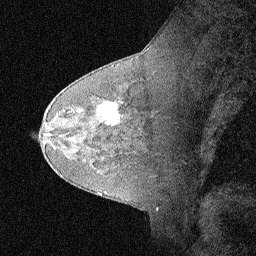
Breast MRI (dynamic contrast-enhanced), one sagittal slice; slice 43 of 64 in the series (ordered by position); dynamic contrast-enhanced study with each time point stored as its own series, time point 2 of 3 at this slice position (early post-contrast, ordered by acquisition time); 1.5 T; TE 4.5 ms, TR 11 ms; 2.06 mm slice thickness; 256 × 256 image matrix, field of view 200 × 200 mm. Female patient, age 62 years. Case-level facts recorded for this patient, not image findings: setting: breast cancer imaged before/during neoadjuvant chemotherapy; receptor status: HR-positive, HER2-negative.
Annotated regions visible in this slice (semi-automatically segmented with operator editing):
- analysis volume of interest (the breast-tissue region the enhancement analysis was run in; not a lesion): bounding box (x1, y1, x2, y2) in pixels: (91, 93, 124, 129)
- tumour enhancement mask (voxels above the 90 % enhancement threshold inside the analysis volume of interest): (100, 101, 119, 124)